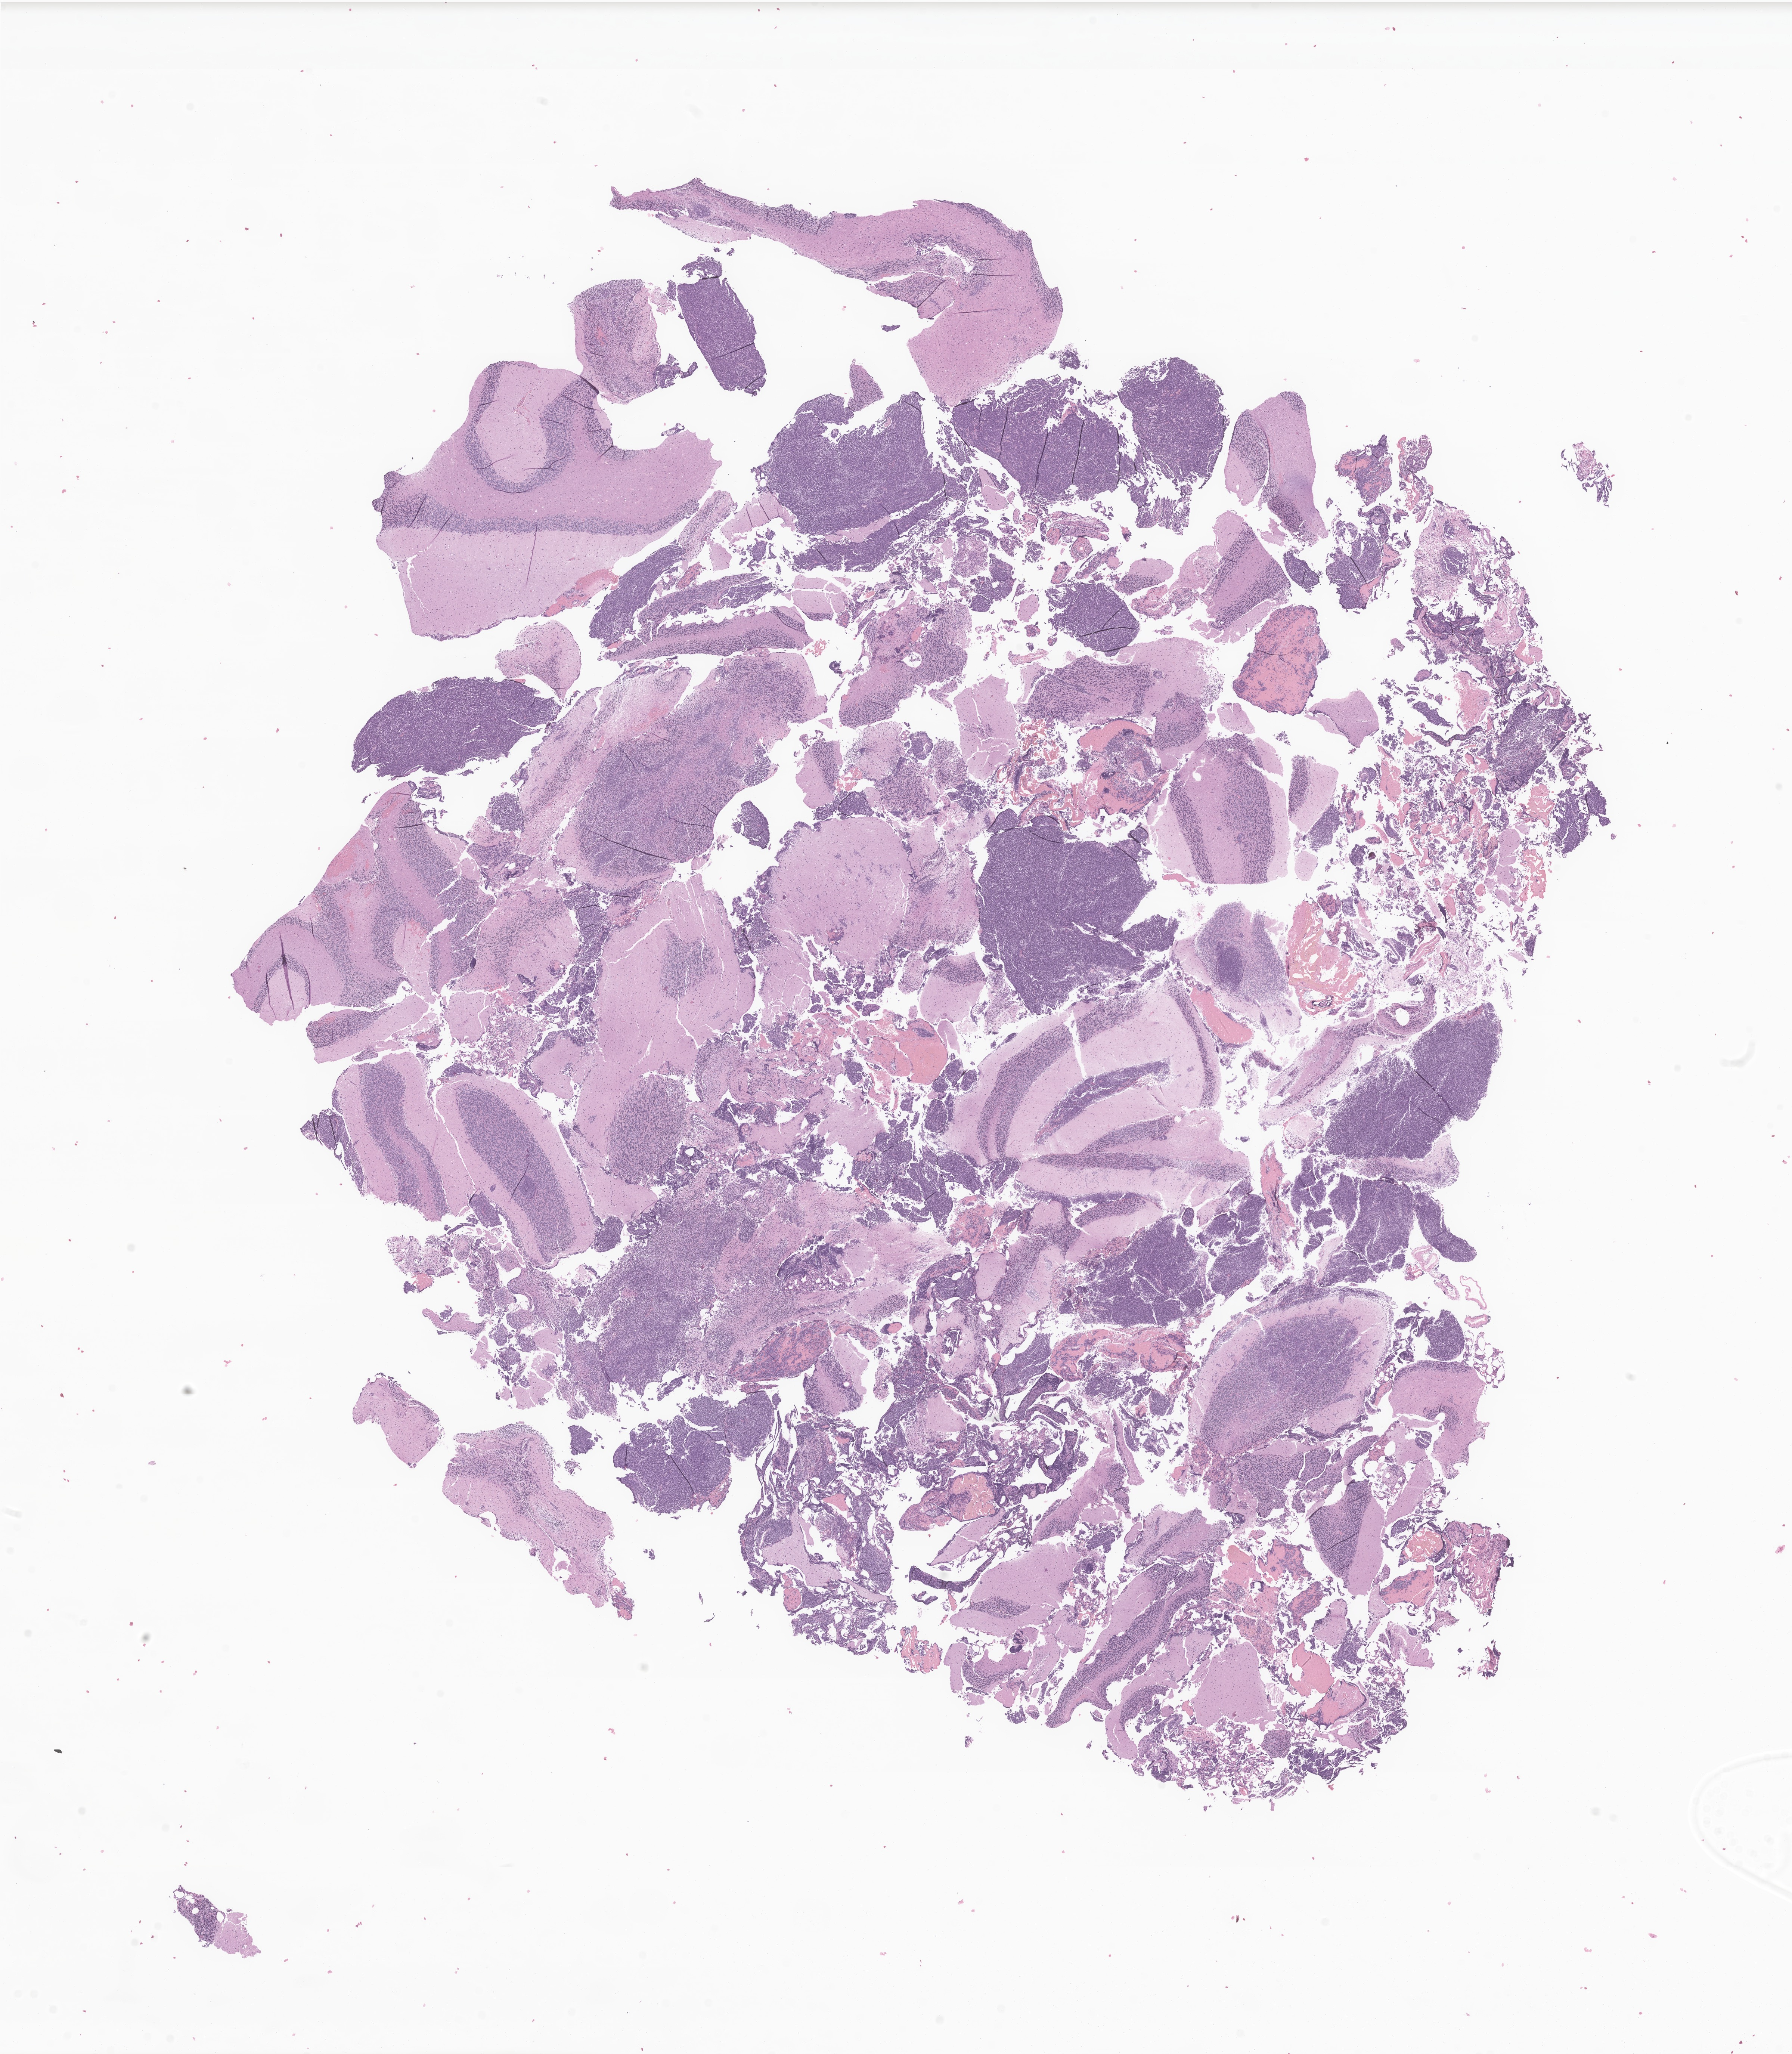
Whole-slide image, haematoxylin and eosin stain of tumor tissue from the cerebellum, low-resolution overview of the scanned area, about 20.2 x 23.2 mm. Formalin-fixed paraffin-embedded section. Female patient, age 182 months (15 years 2 months).
Recorded diagnosis: Medulloblastoma, NOS.